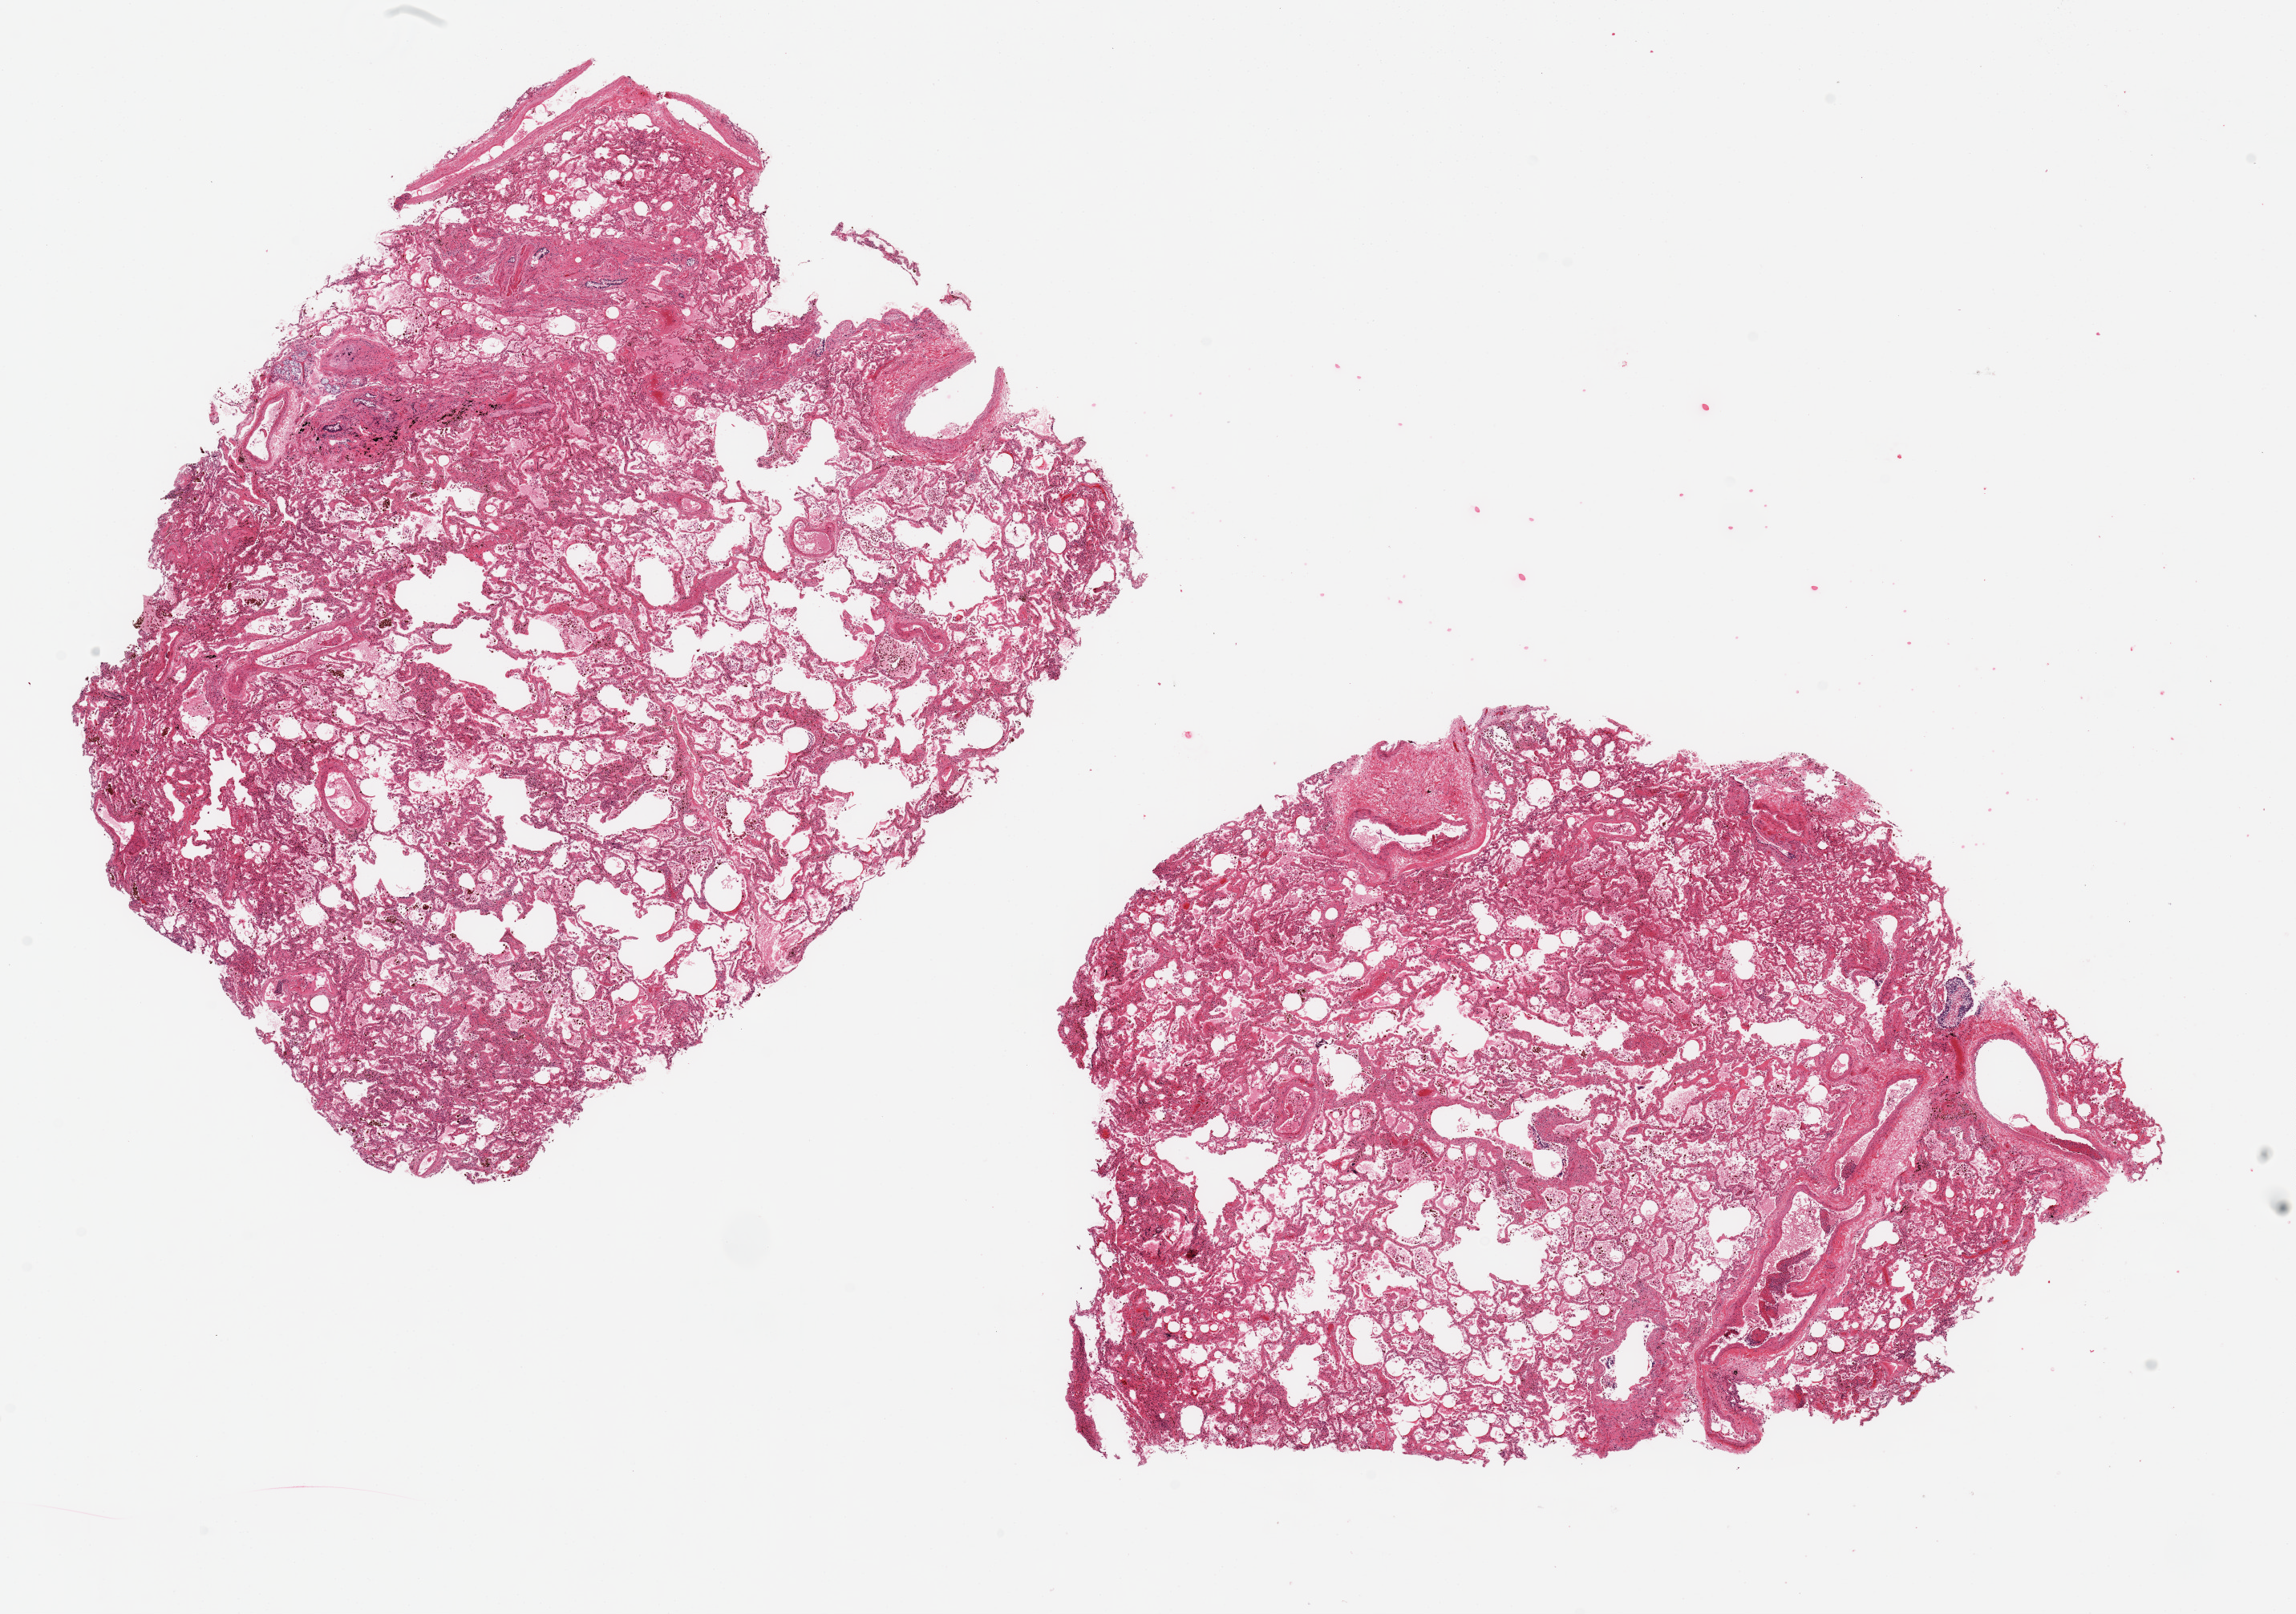
H&E whole-slide image, brightfield, a low-resolution overview of the entire scanned area, about 22.6 x 15.9 mm, PAXgene-fixed paraffin-embedded (PFPE) section, sampled site (target tissue): lung, tissue donor sample. Donor sex: female.
Reviewer comment on this tissue sample: 2 ~9.5x8mm aliquots; mild congestion, occasional prominent aggregates of hemosiderin-laden macrophages.